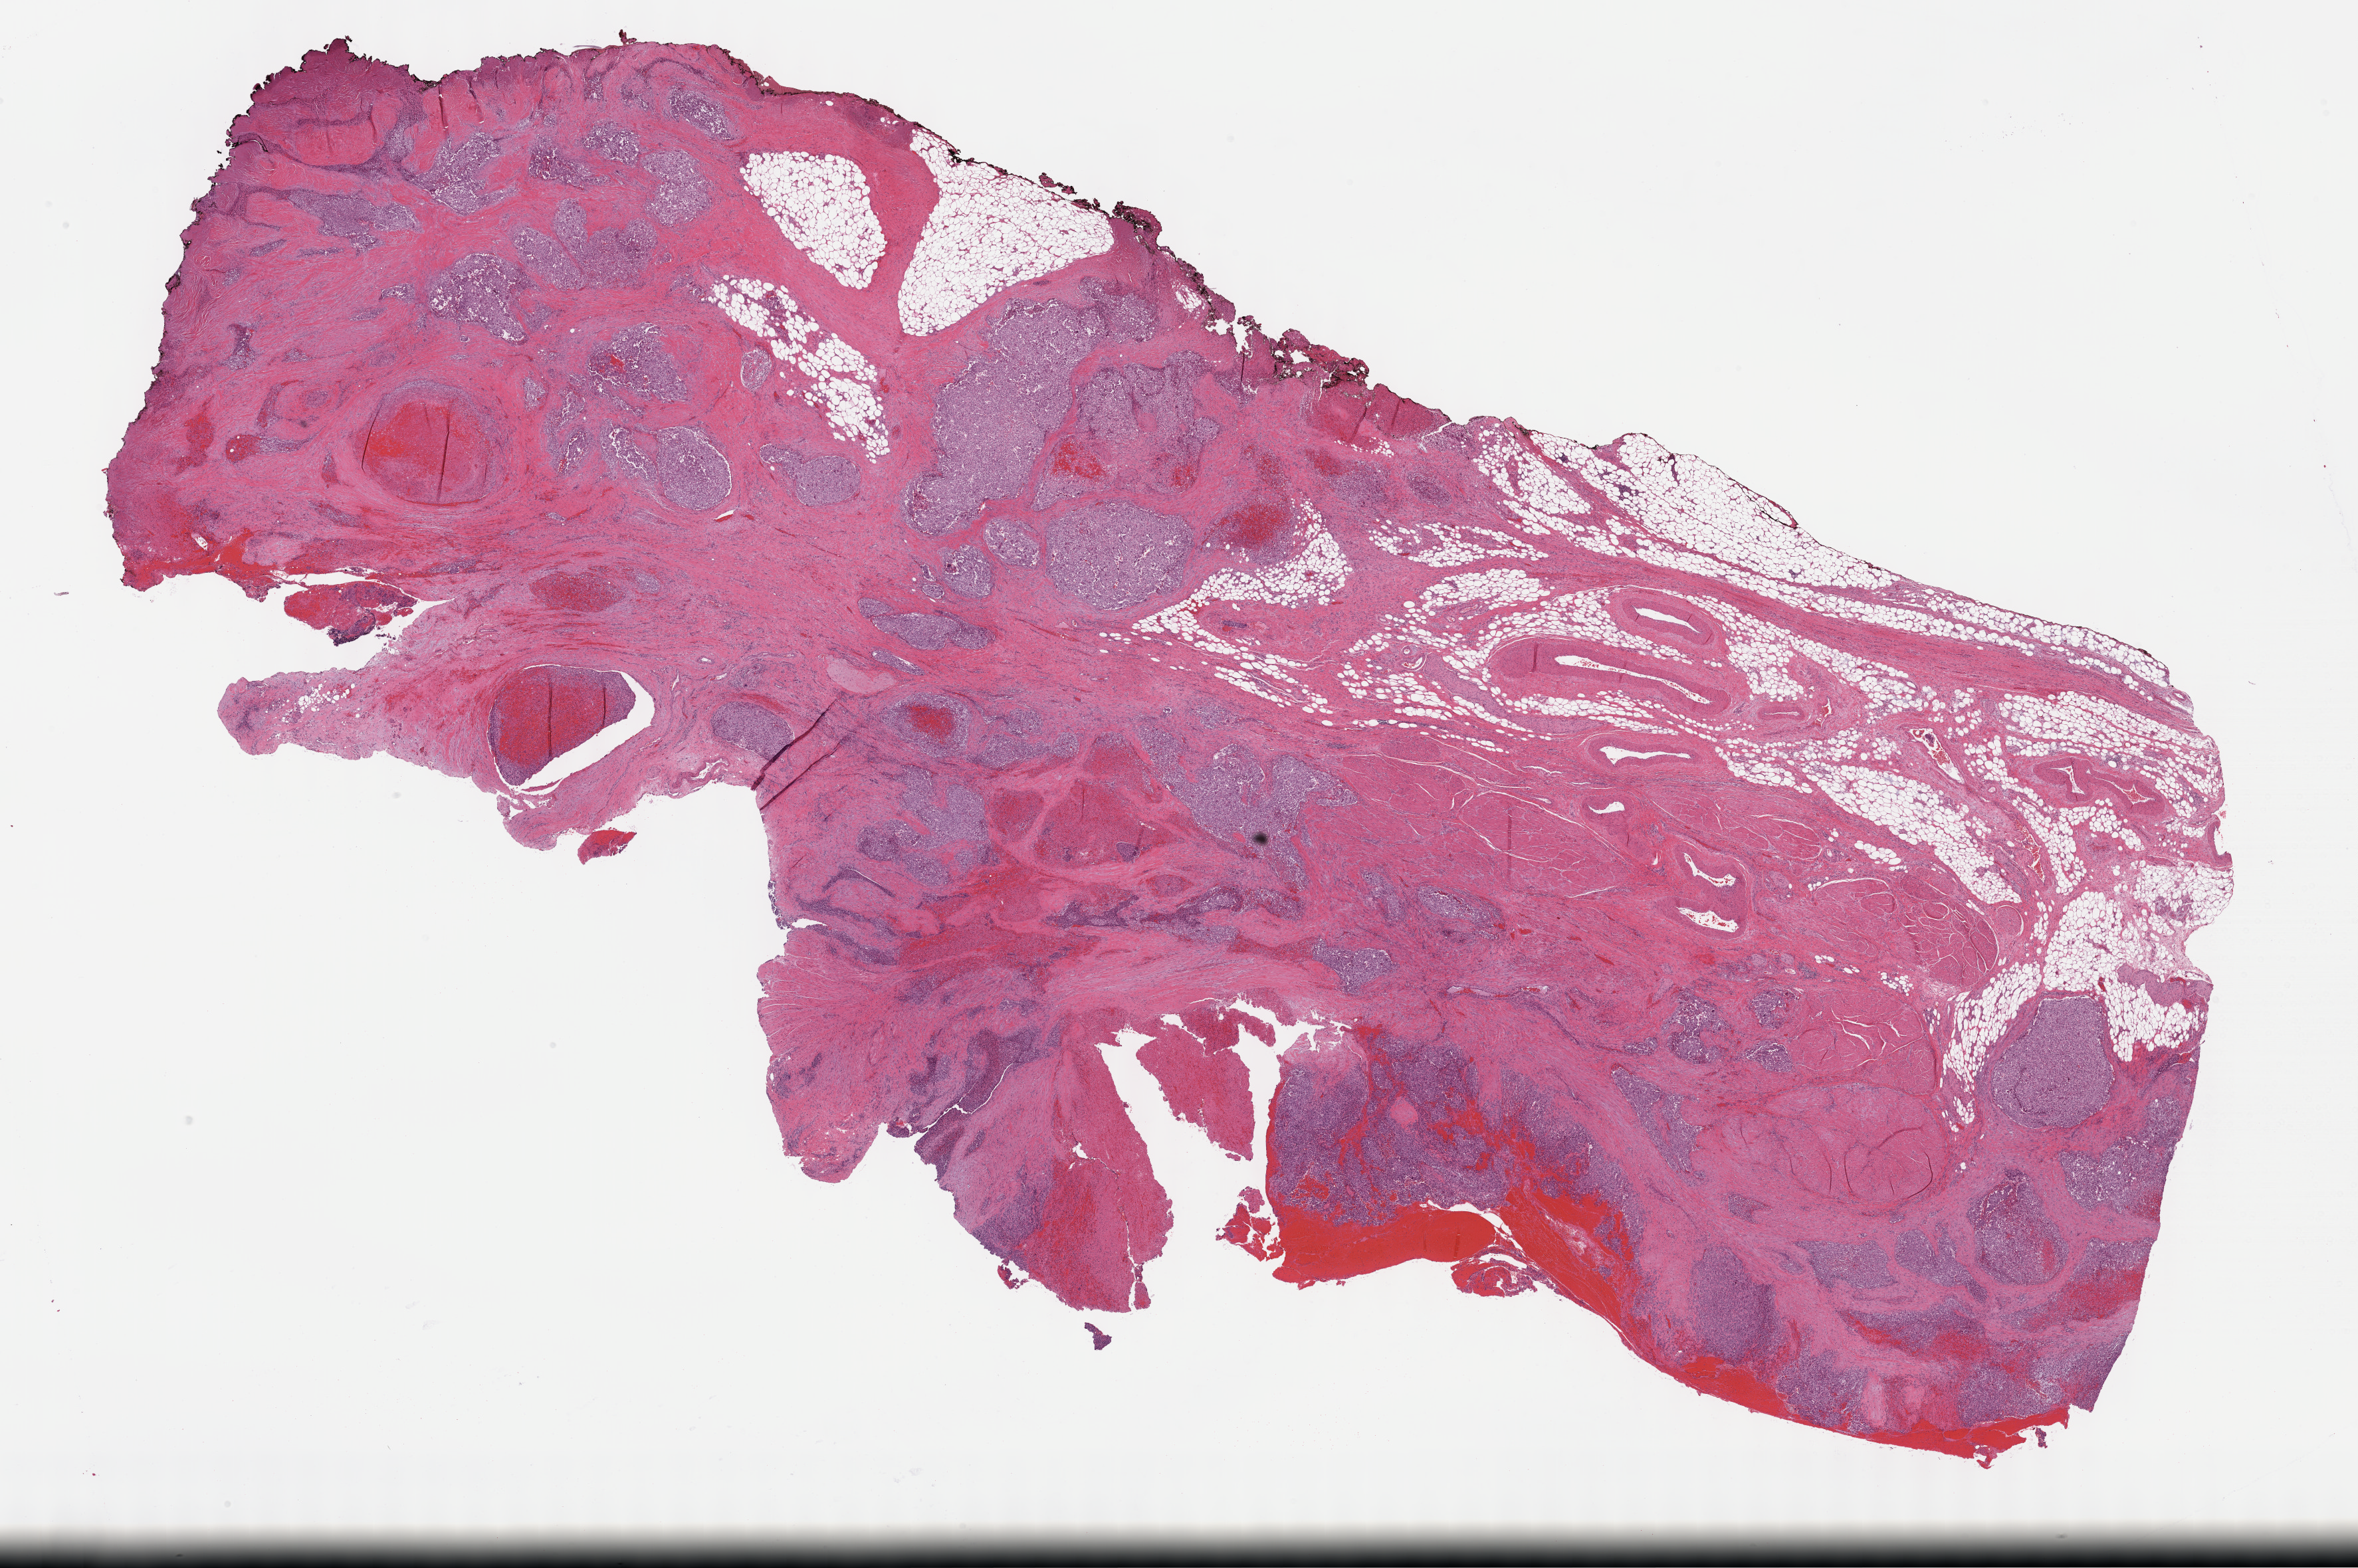
Digitized H&E tissue section (whole slide) — shown as a low-resolution overview of the whole scanned area (about 28.7 x 19.1 mm). Formalin-fixed paraffin-embedded (FFPE) diagnostic section. Bladder, primary tumour sample. Patient: male, age at initial diagnosis 82 years. Histologic grade: high grade.
Diagnosis: Transitional cell carcinoma (posterior wall of bladder). Lymph nodes positive (case pathology): 1 of 8 examined. AJCC pathologic stage: IV.